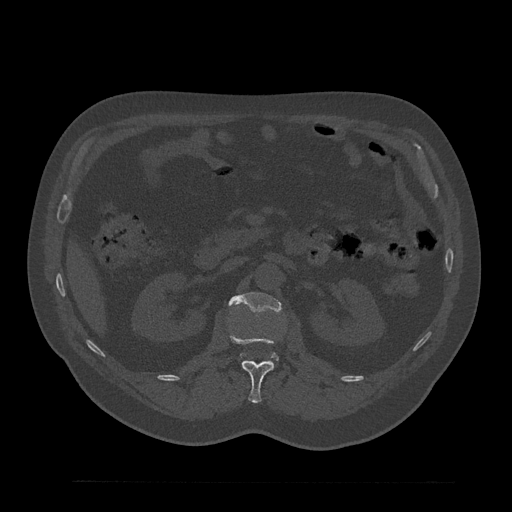
CT including the spine, one axial slice; reconstruction kernel Br40s/3; 120 kVp; bone window (W 1800 / L 400 HU); 0.5 mm slice thickness; 512 × 512 image matrix. Male patient, age 61 years. Case-level facts recorded for this patient, not image findings: primary cancer: prostate.
Annotated regions visible in this slice (semi-automatically segmented with operator editing):
- L1 vertebra: bounding box (x1, y1, x2, y2) in pixels: (230, 334, 276, 404)
- L2 vertebra: (228, 292, 282, 358)